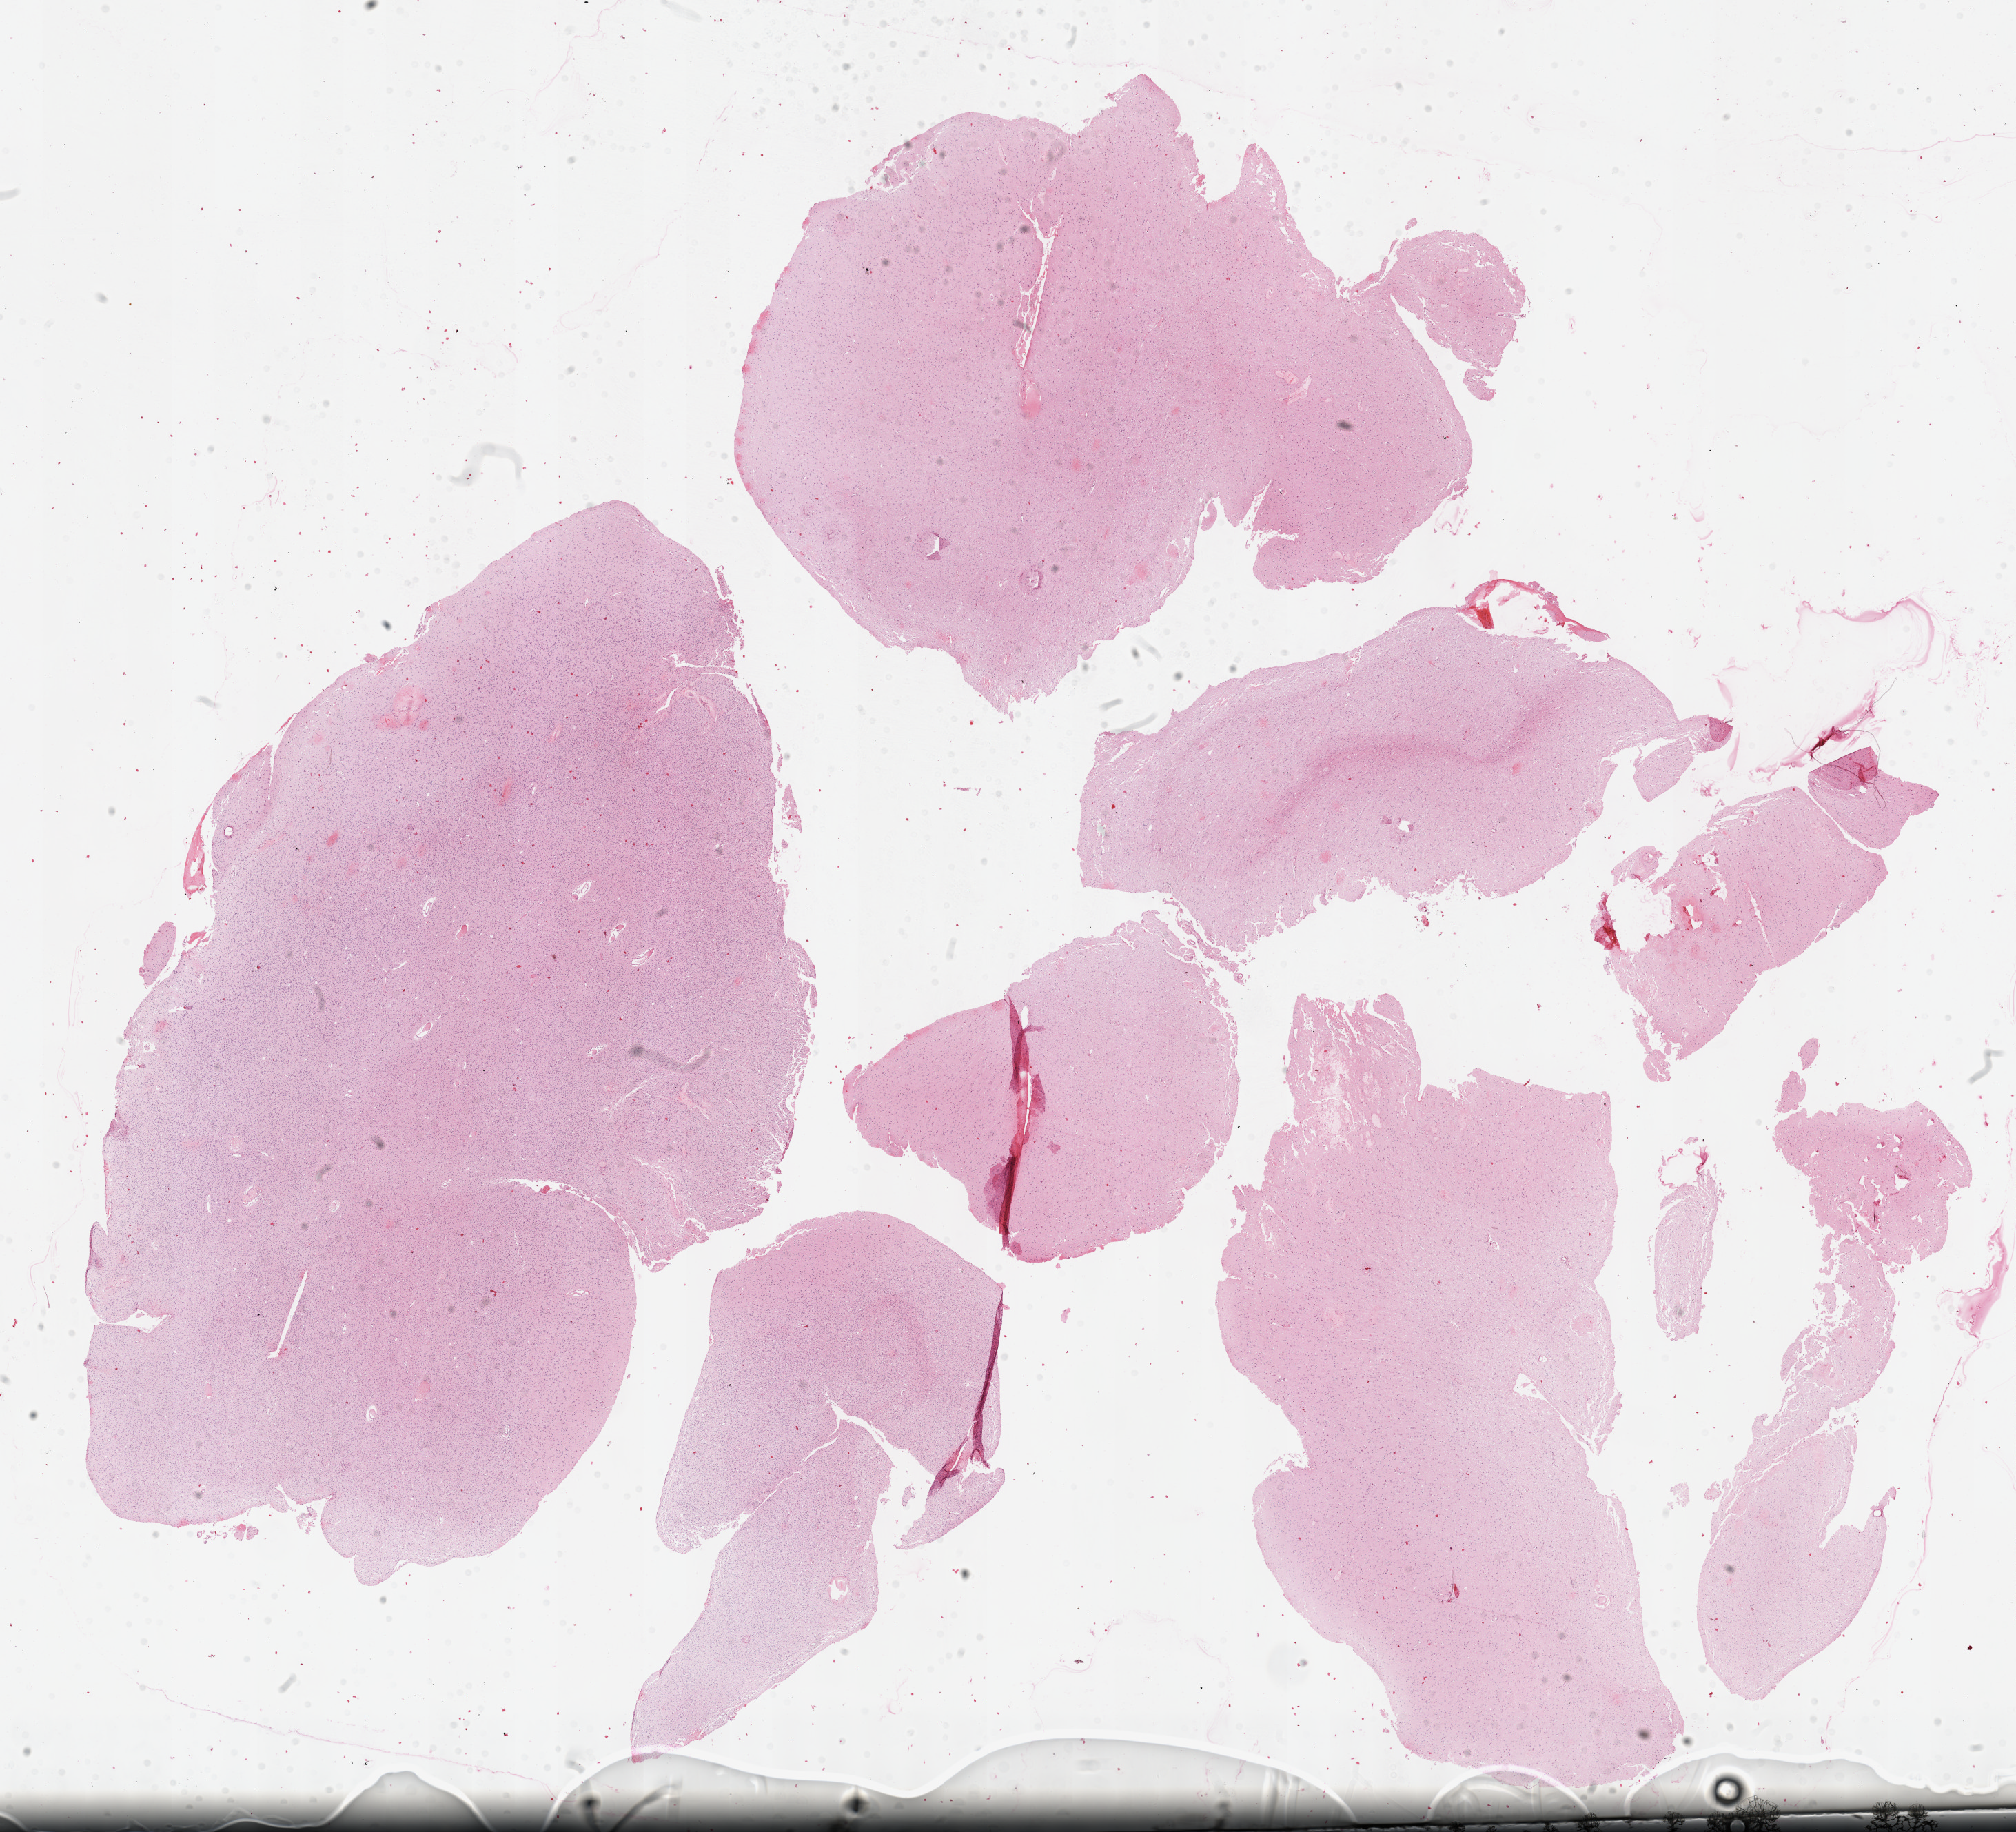
Whole-slide histology image, H&E, shown as a low-resolution overview of the whole scanned area (about 23.7 x 21.5 mm). FFPE section. Sample: primary tumour, brain. Female, age 58 years at initial diagnosis. Histologic grade: G2 (moderately differentiated).
Diagnosis: Mixed glioma (cerebrum). Laterality: left.